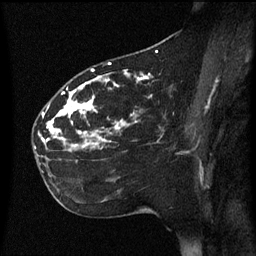
Breast MRI (dynamic contrast-enhanced), one sagittal slice. Slice 32 of 60 in the series (ordered by position). Dynamic contrast-enhanced series, image 2 of 3 at this slice position (ordered by acquisition). 1.5 T. TE 4.2 ms, TR 8.4 ms. 2.2 mm slice thickness. 256 × 256 image matrix. Patient: female, 35 years. From the clinical record (not read from this slice): setting: breast cancer imaged before/during neoadjuvant chemotherapy; receptor status: HER2-positive.
Outlined on this slice (semi-automatic segmentation, software-assisted and operator-edited):
- analysis volume of interest (the breast-tissue region the enhancement analysis was run in; not a lesion): bounding box <33,78,173,163> (left, top, right, bottom; pixels)
- tumour enhancement mask (voxels above the 70 % enhancement threshold inside the analysis volume of interest): <35,78,147,149>